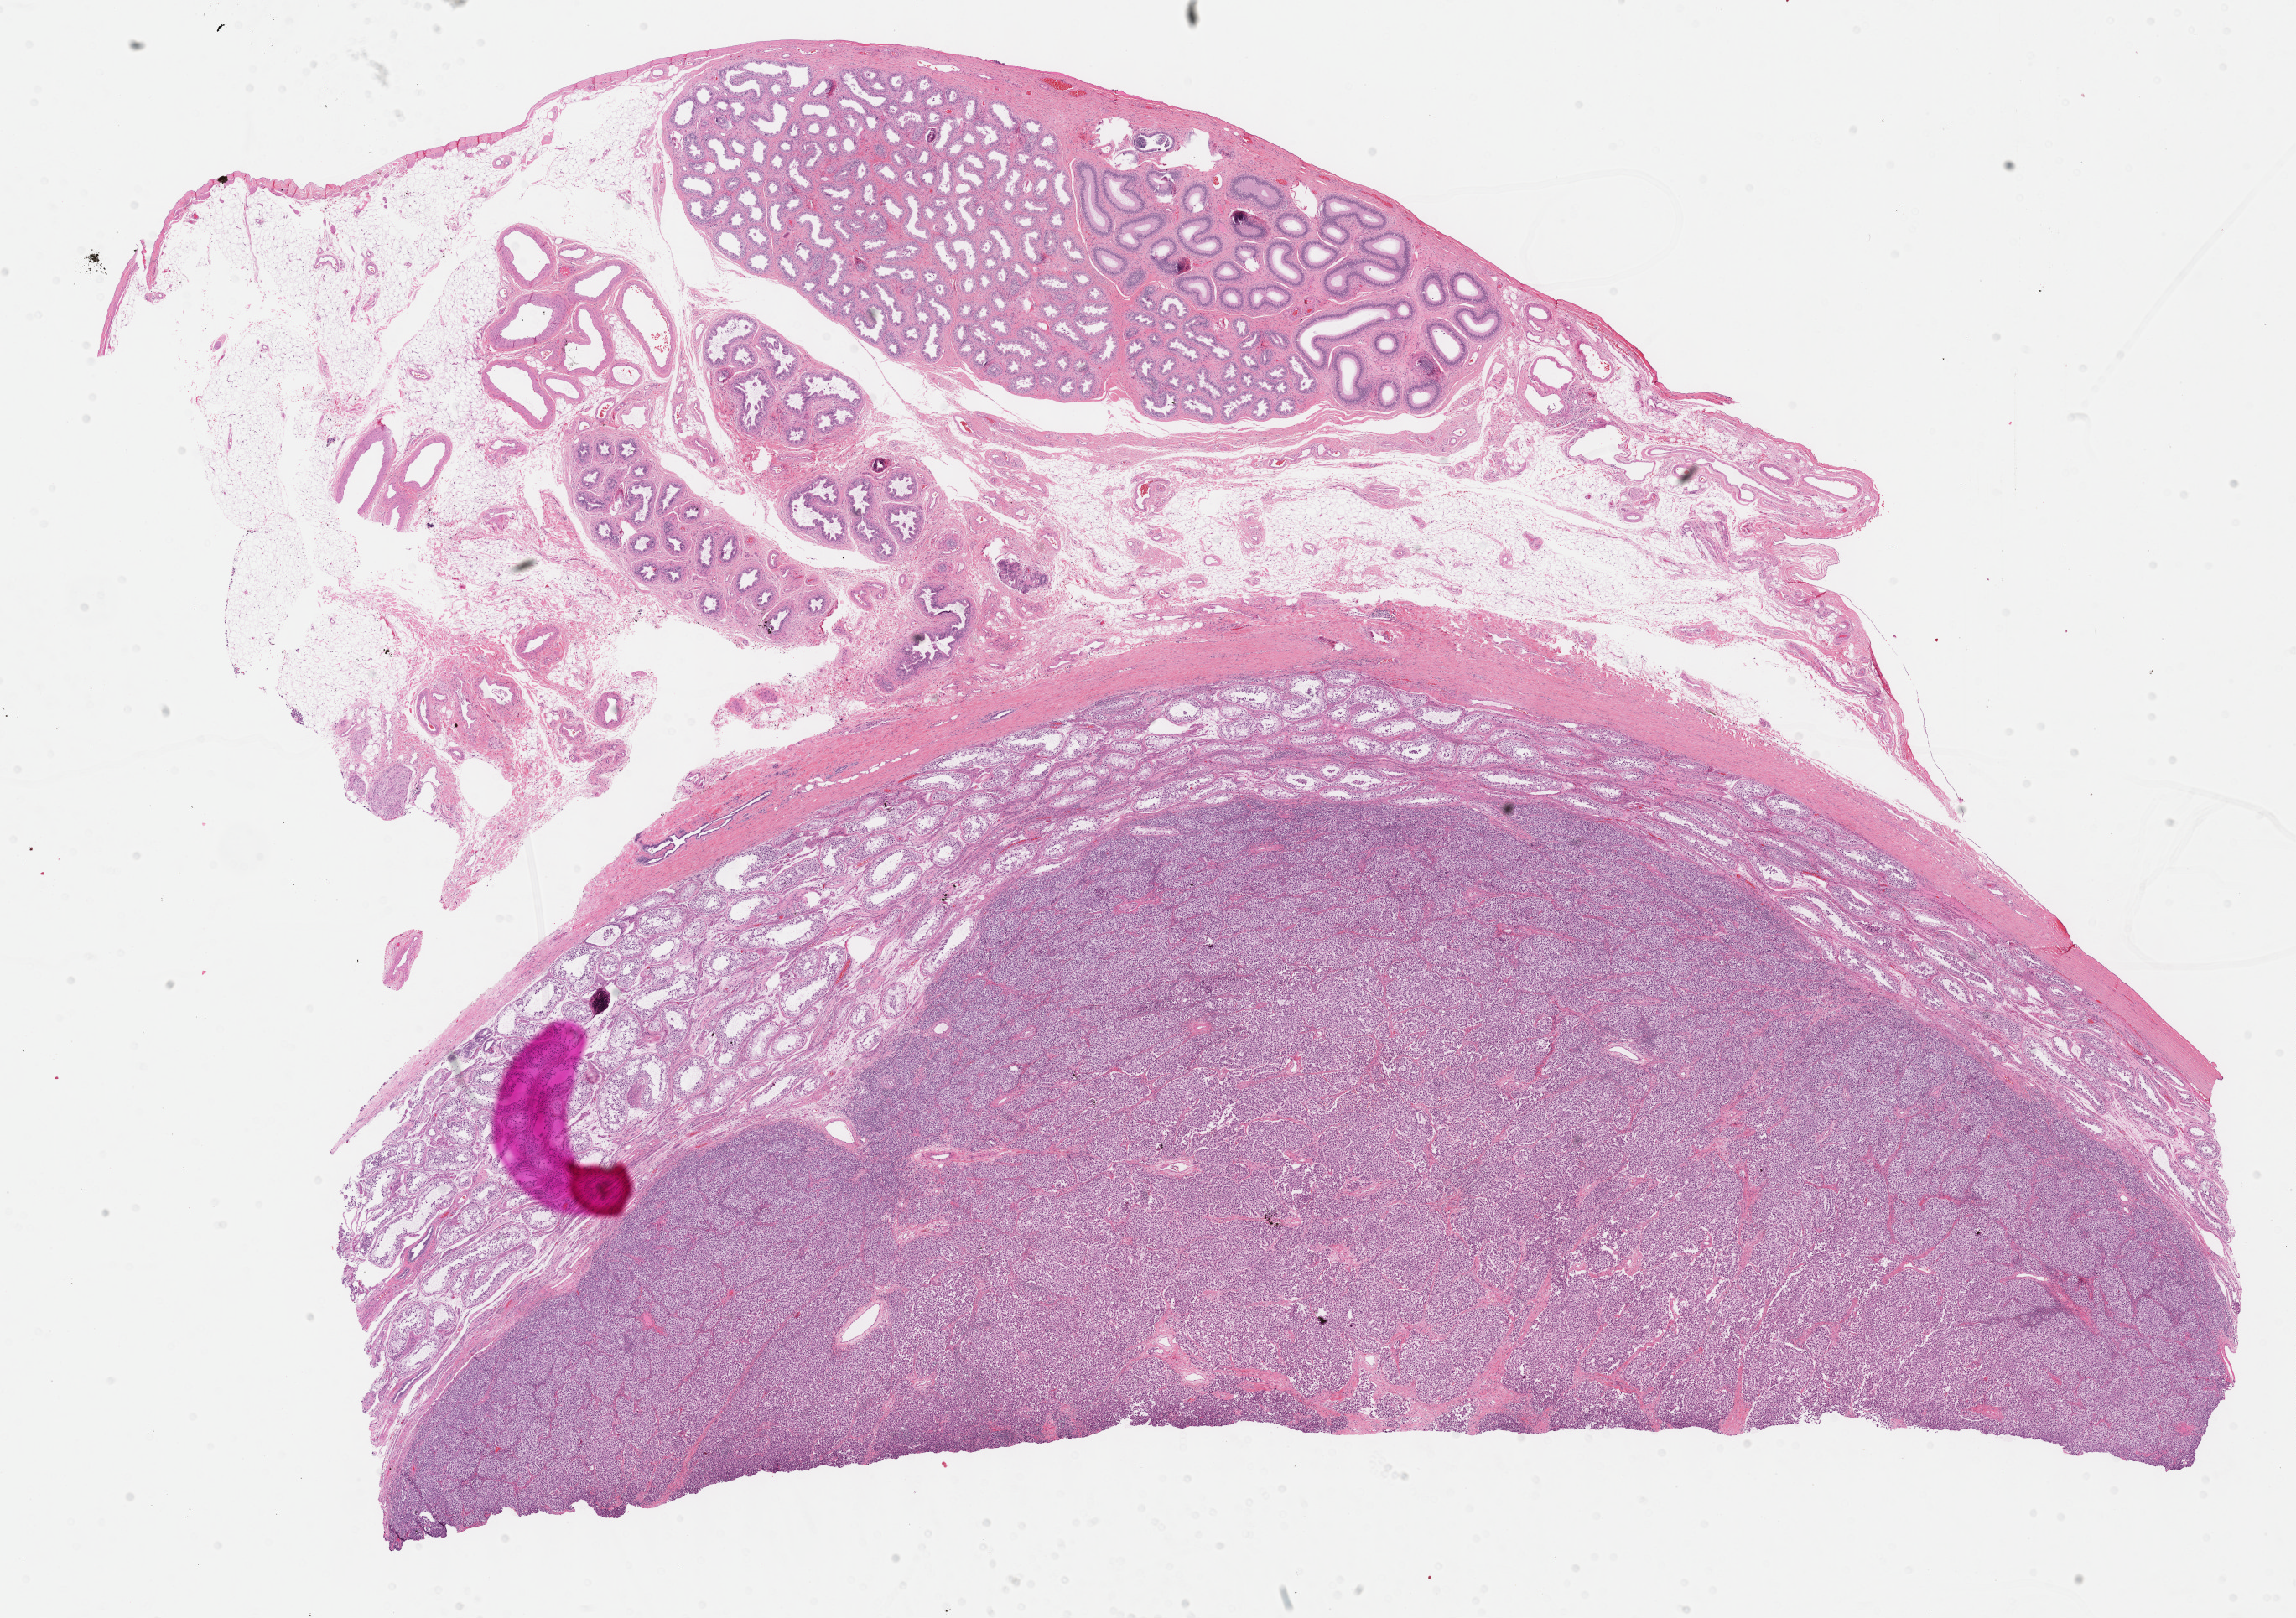
Digitized Hematoxylin and eosin (H&E) stained tissue section (whole slide) — low-resolution overview of the scanned area, about 22.1 x 15.6 mm, formalin-fixed paraffin-embedded (FFPE) diagnostic section, testis, primary tumour sample. Male patient; age at initial diagnosis 38 years.
Histologic diagnosis: Seminoma, NOS. Laterality: left.